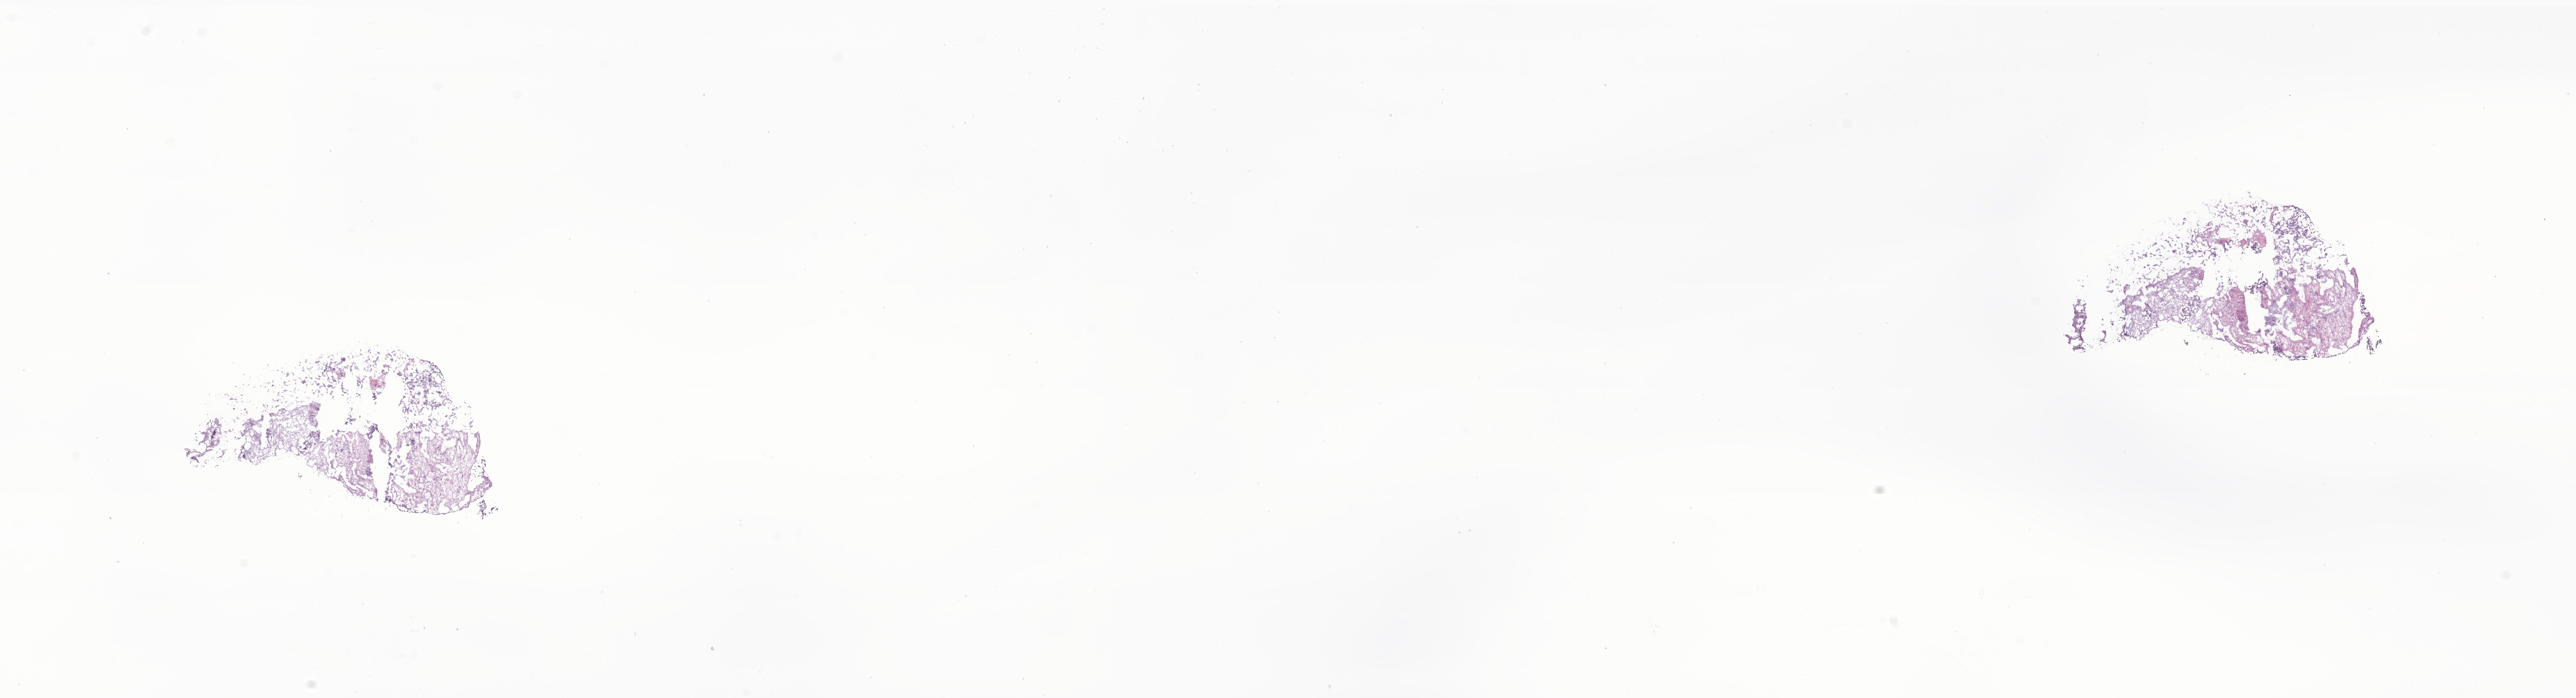
Whole-slide image, hematoxylin and eosin (H&E) stain of tumor tissue from the liver — a low-resolution overview of the entire scanned area, about 26.2 x 7.1 mm. Frozen section (OCT-embedded). Male patient, age 237 months (19 years 9 months).
* recorded diagnosis: Neoplasm, malignant